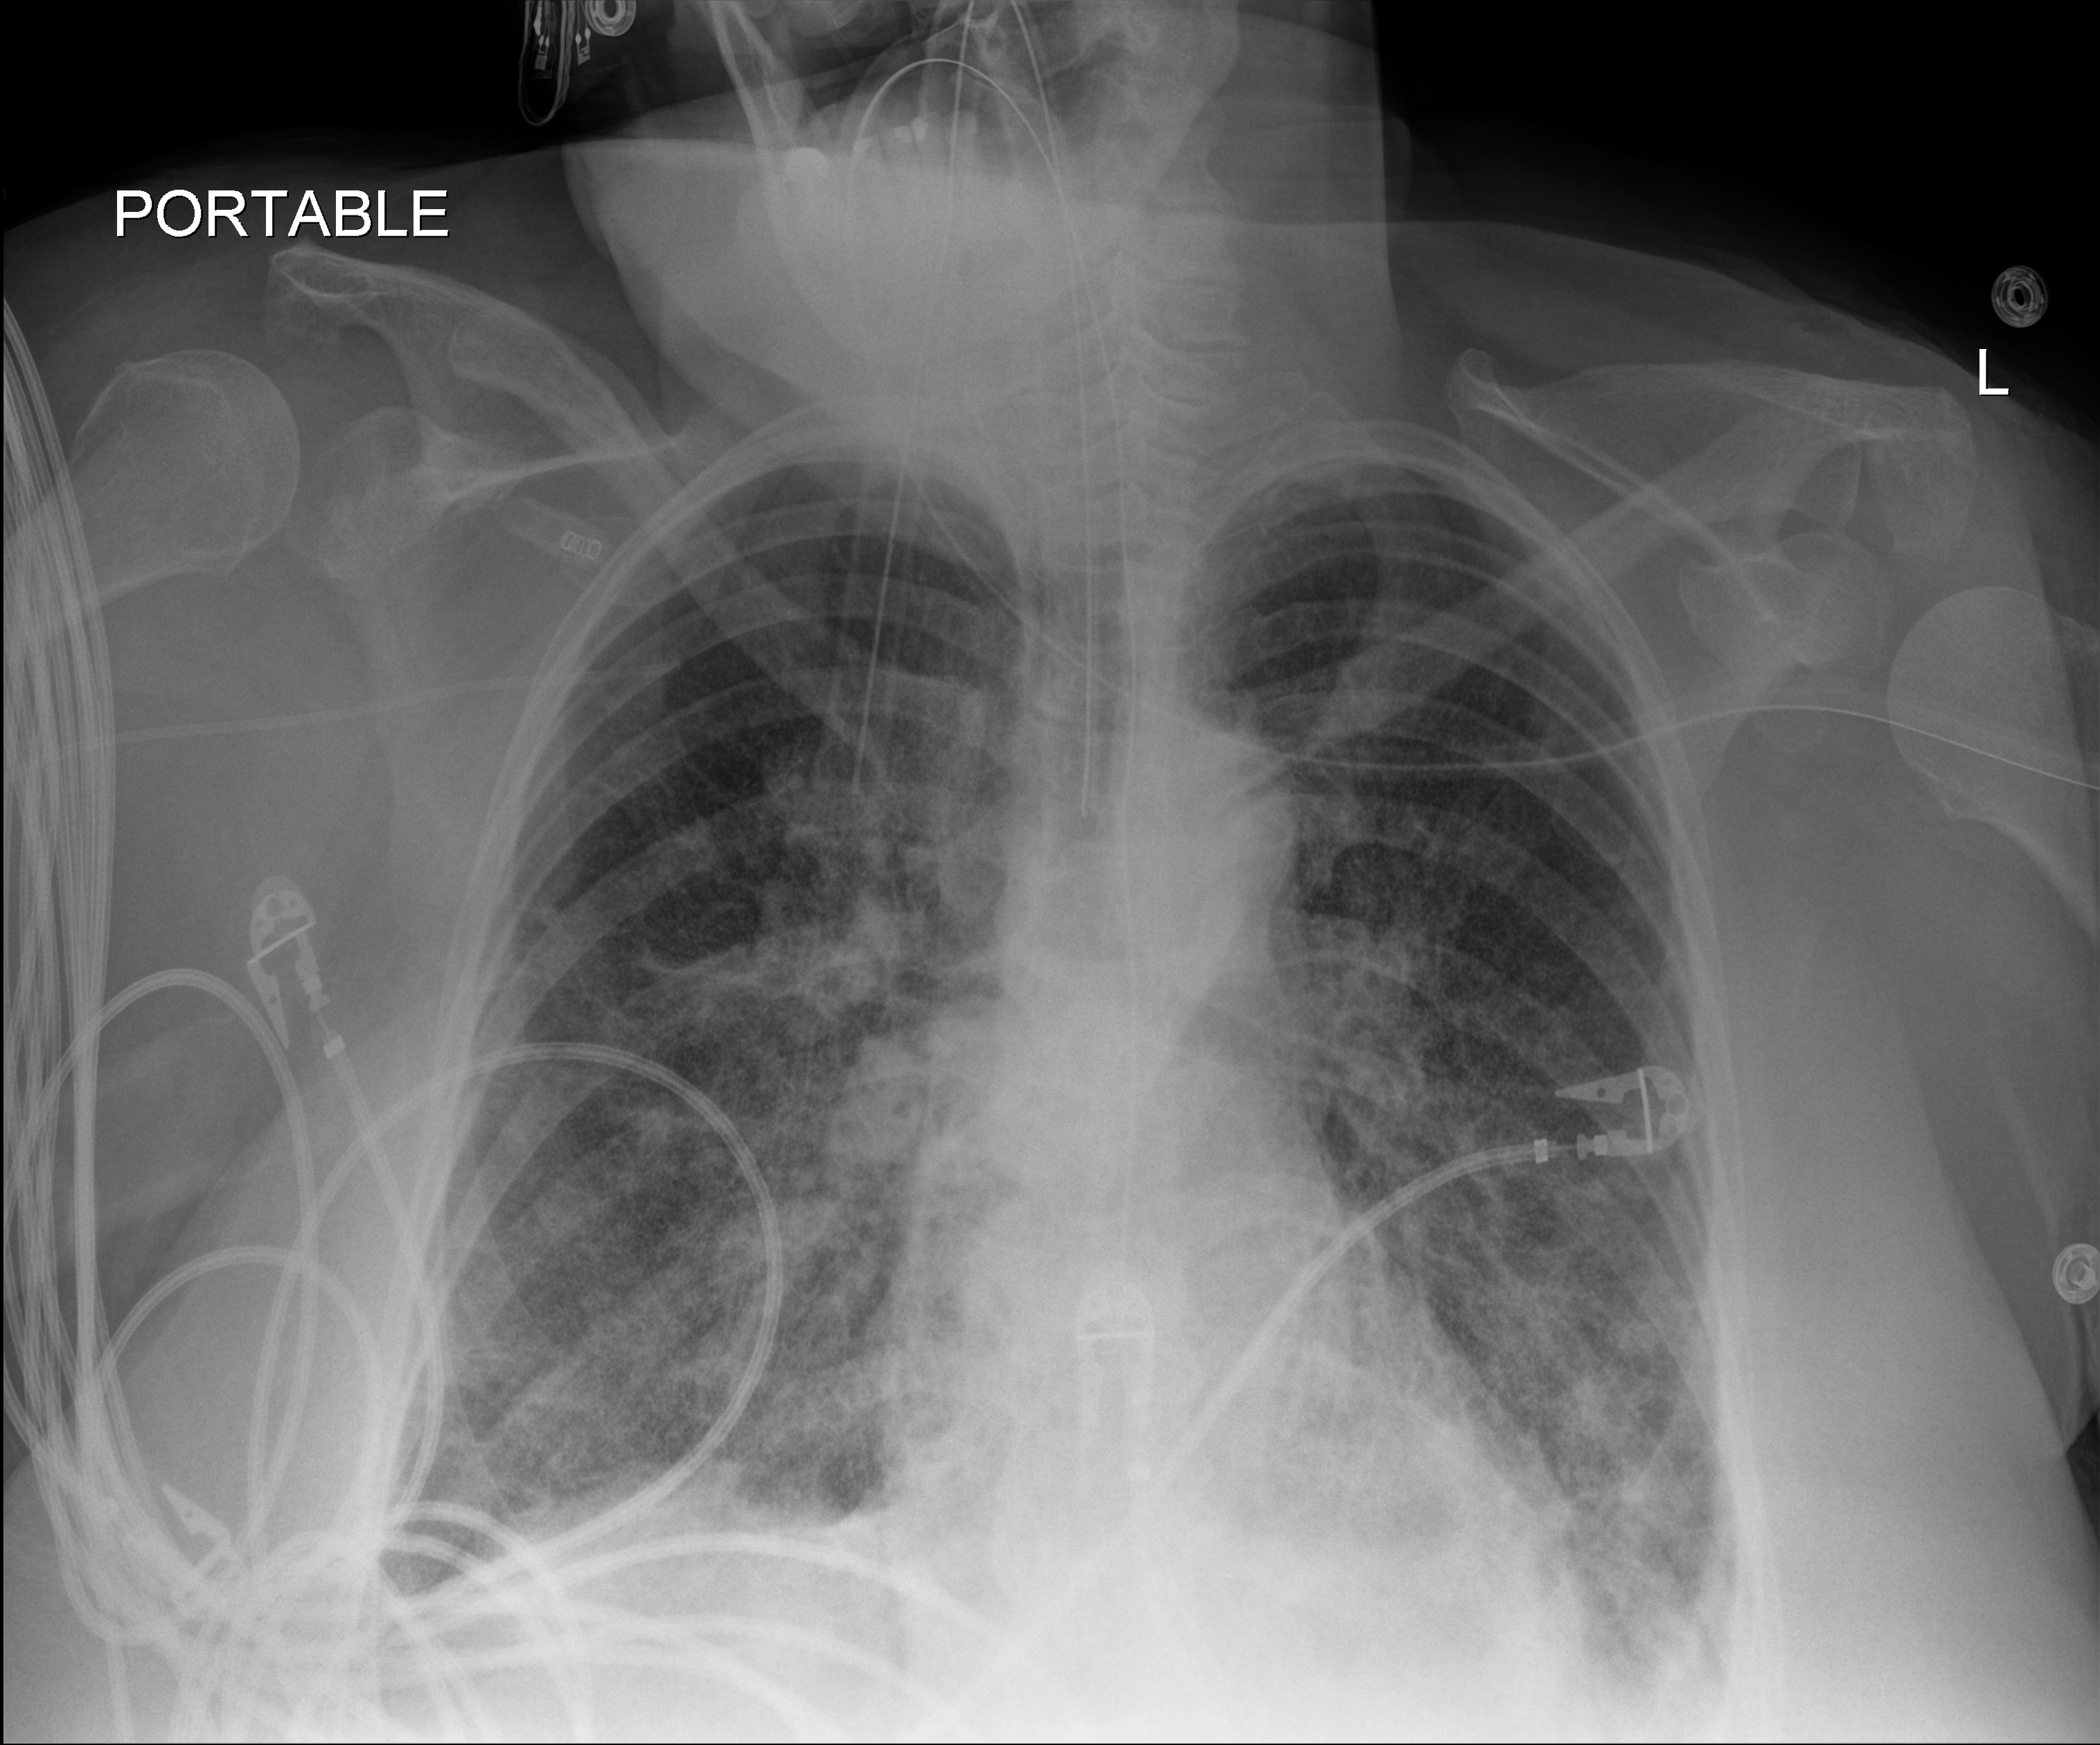
Chest X-ray (portable). Patient hospitalised with COVID-19; female, aged 60–74 years.
From the hospital-stay record, not from the radiograph (when in the stay this image was taken is not recorded):
- mechanically ventilated during this hospital stay: yes
- admitted to intensive care during this hospital stay: yes